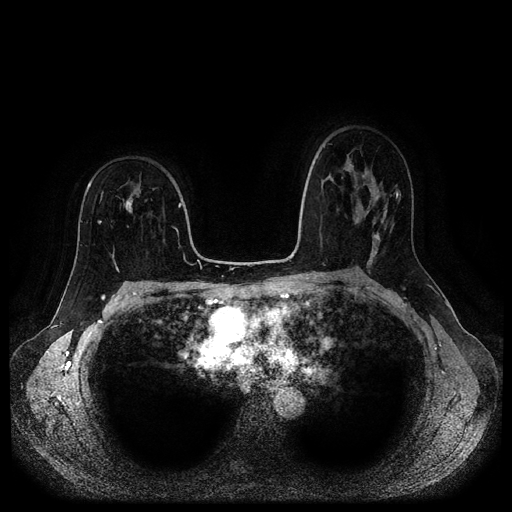
Breast MRI (dynamic contrast-enhanced, multi-phase), one axial slice; slice 64 of 116 in the series (ordered by position); dynamic contrast-enhanced series, time point 2 of 5 at this slice position (early post-contrast); 1.5 T; TE 2.6 ms, TR 5.3 ms; 2 mm slice thickness; 512 × 512 image matrix, field of view 360 × 360 mm. Female patient, age 50 years.
Annotated regions visible in this slice (semi-automatically segmented with operator editing):
- breast lesion (labelled benign in the annotation): box from (x=119, y=184) to (x=142, y=214) px